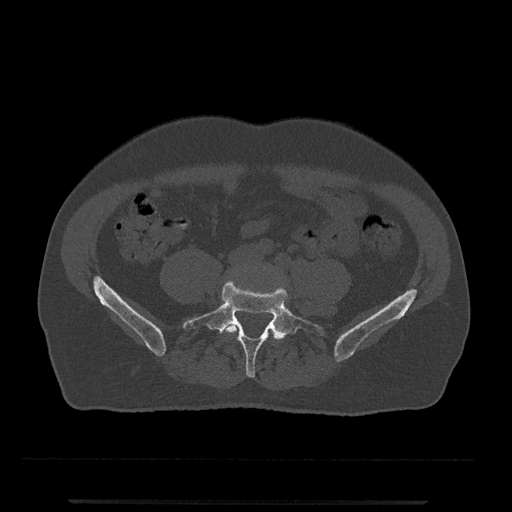
CT including the spine, one axial slice; position 85 of 797 along the scan axis; reconstruction kernel Br40s/3; bone window (W 1800 / L 400 HU); 512 × 512 image matrix, field of view 419 × 419 mm. Male patient, age 63 years. Case-level facts recorded for this patient, not image findings: primary cancer: prostate.
Structures marked on this image (semi-automatic segmentation, software-assisted and operator-edited):
- L4 vertebra: bounding box (x1, y1, x2, y2) in pixels: (224, 320, 274, 335)
- L5 vertebra: (182, 281, 324, 378)